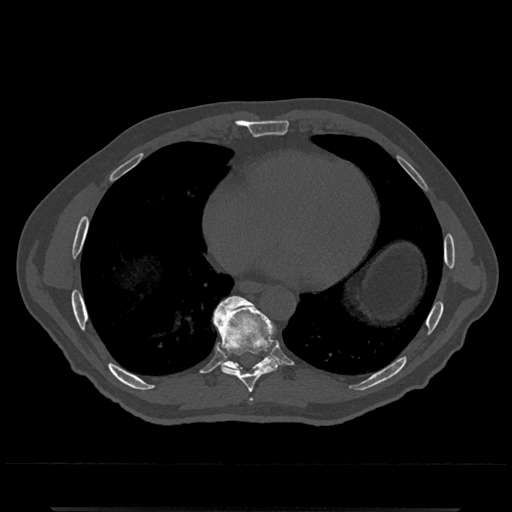
CT including the spine, one axial slice; position 649 of 797 along the scan axis; reconstruction kernel Br40s/3; 120 kVp; bone window (W 1800 / L 400 HU); 0.5 mm slice thickness; 512 × 512 image matrix, field of view 393 × 393 mm. Male patient, age 67 years. Case-level facts recorded for this patient, not image findings: primary cancer: prostate.
Annotated regions visible in this slice (semi-automatically segmented with operator editing):
- T8 vertebra: bounding box [x1, y1, x2, y2] px = [214, 301, 279, 393]
- T9 vertebra: [212, 295, 277, 371]